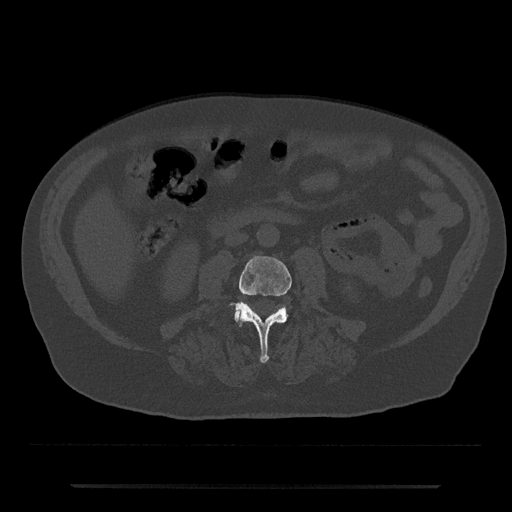
CT including the spine, one axial slice; position 401 of 797 along the scan axis; 120 kVp; bone window (W 1800 / L 400 HU); 0.5 mm slice thickness; 512 × 512 image matrix. Male patient, age 80 years. Case-level facts recorded for this patient, not image findings: primary cancer: prostate.
Outlined on this slice (semi-automatic segmentation, software-assisted and operator-edited):
- L3 vertebra: box from (x=231, y=256) to (x=292, y=363) px
- L4 vertebra: (x=234, y=306)–(x=286, y=321)